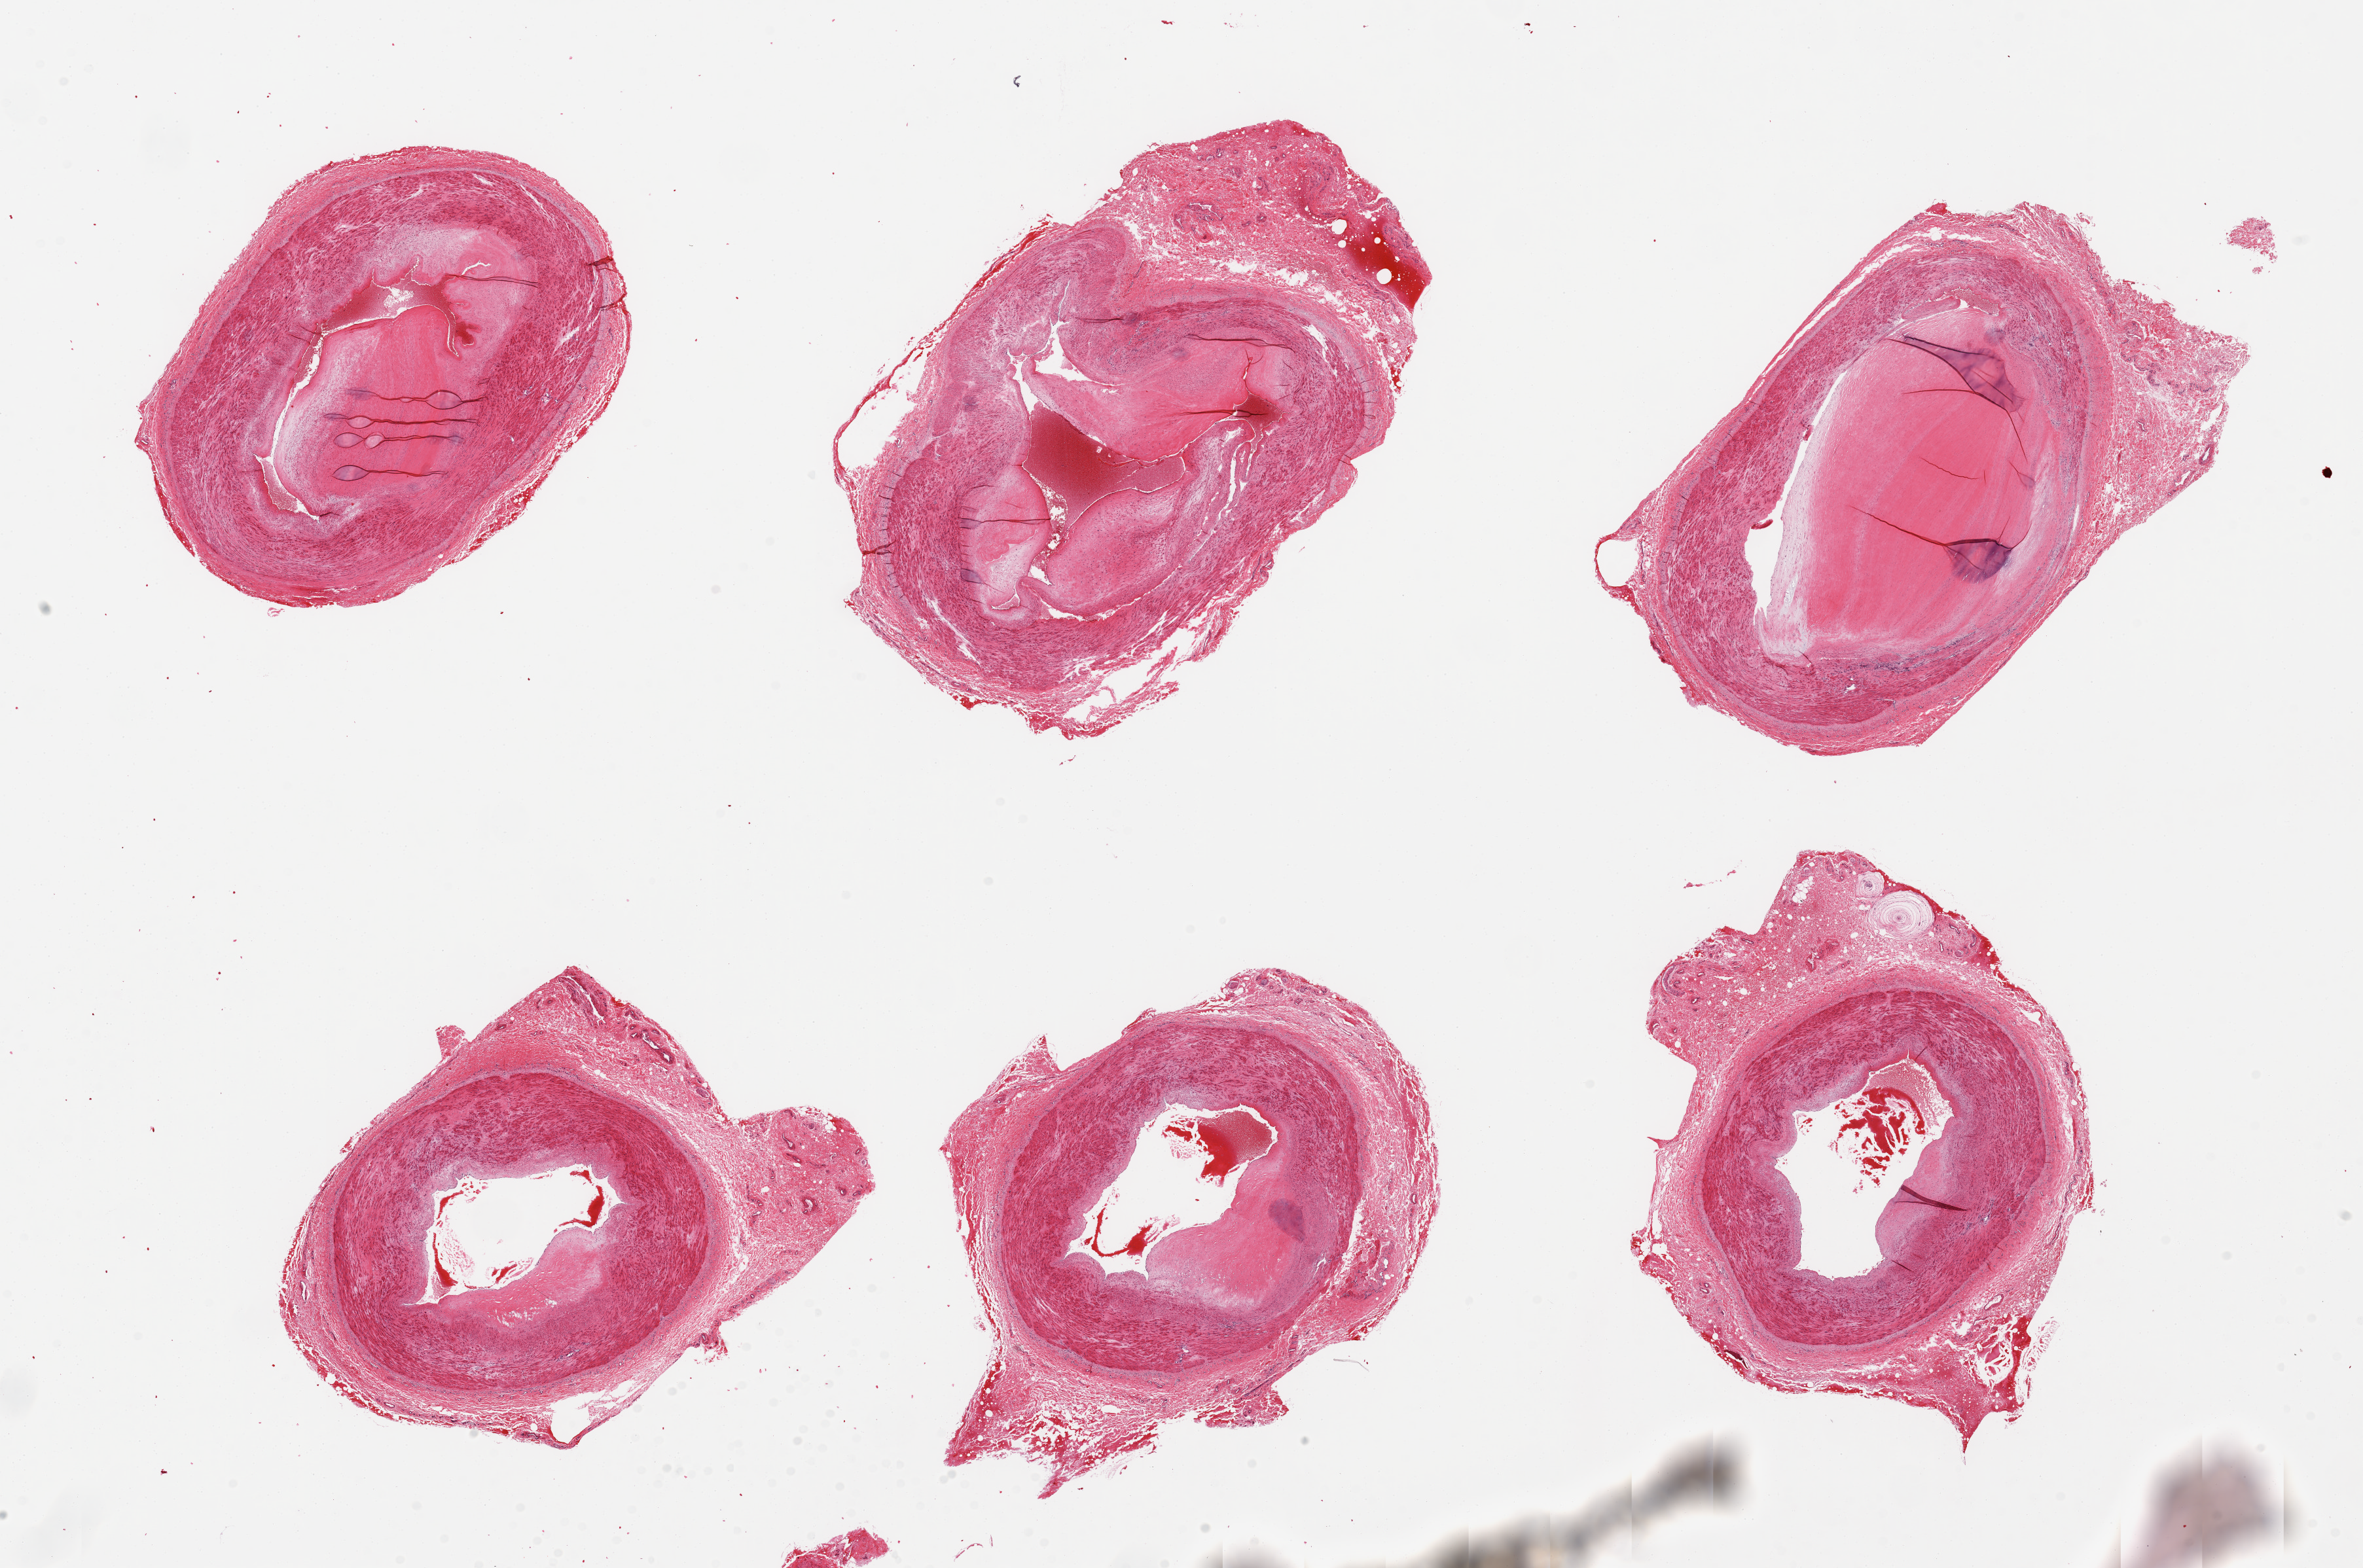
H&E whole-slide image — shown as a low-resolution overview of the whole scanned area (about 28.5 x 18.9 mm, from a 20x scan); PAXgene-fixed paraffin-embedded (PFPE) section; sampled site (target tissue): tibial artery; tissue donor sample. Donor sex: male.
Reviewer comment on this tissue sample: 6 pieces, atherosclerosis with up to near total occlusion of vessel, pacinian corpuscle identified.